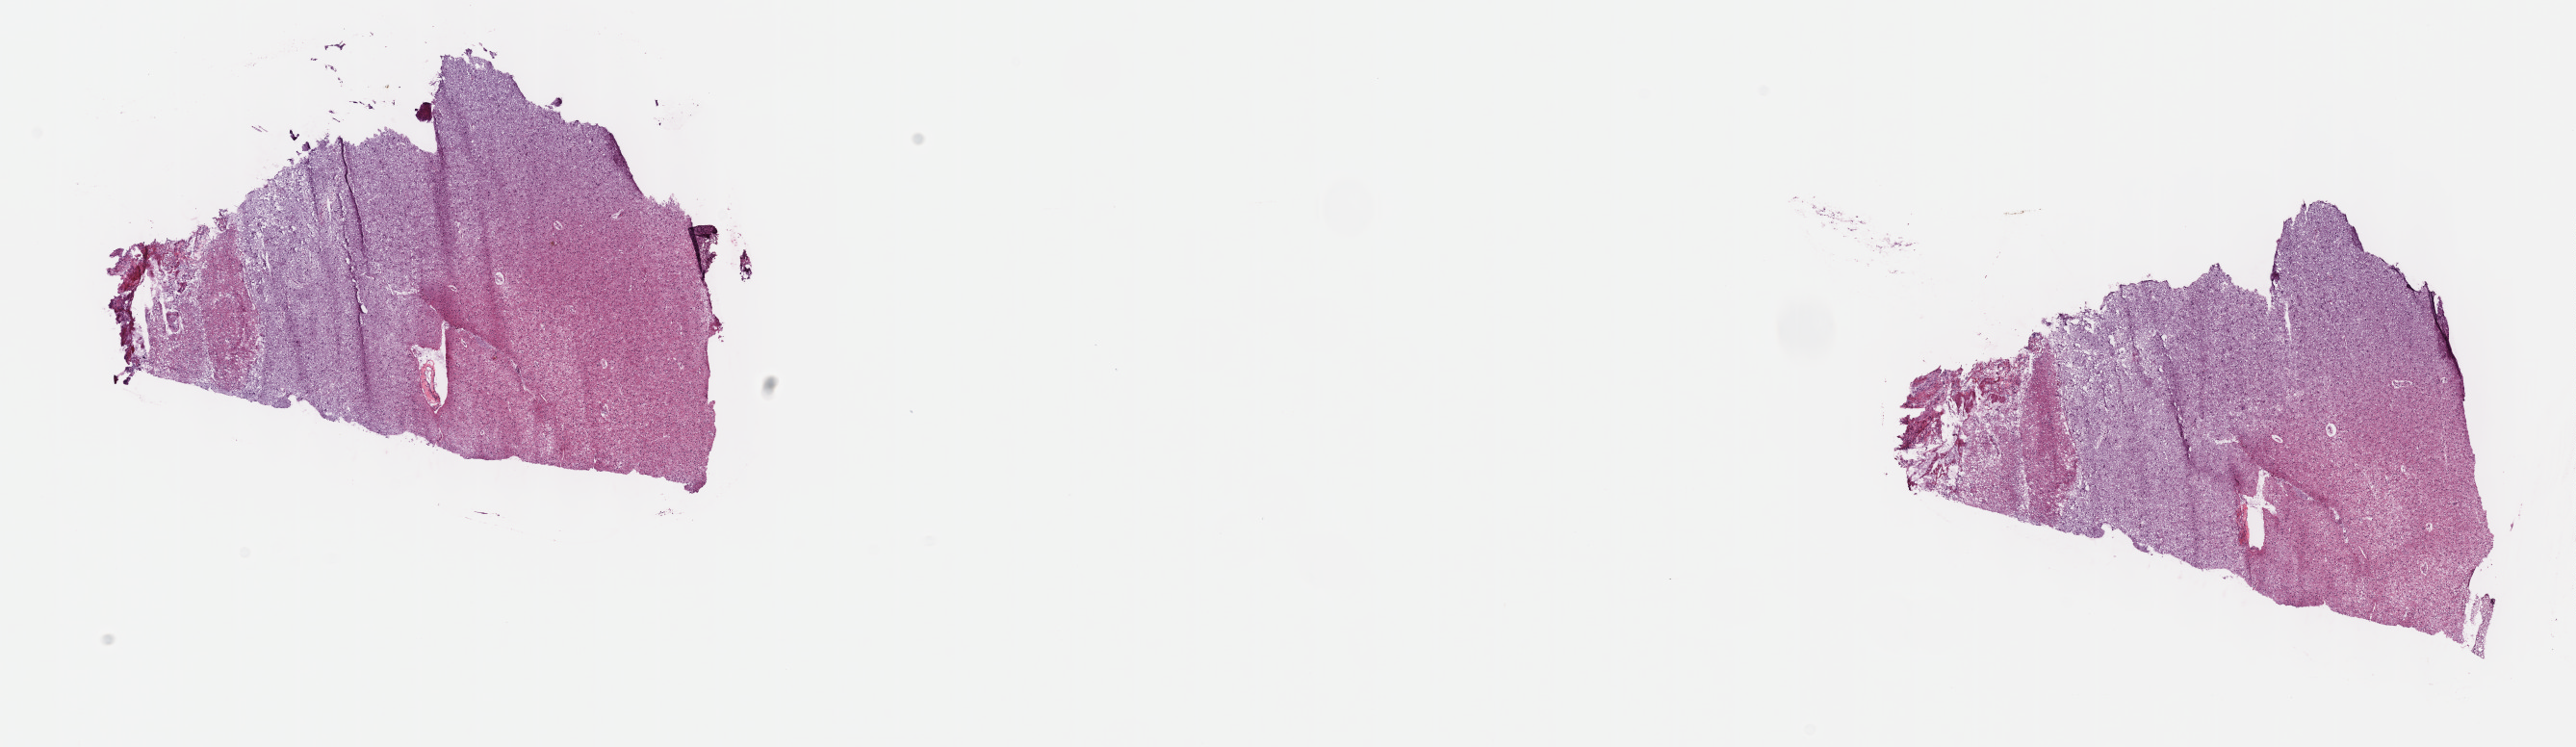
H&E whole-slide image, low-resolution overview of the scanned area, about 21.6 x 6.3 mm (from a 40x scan); frozen section; primary tumour sample from the brain. Male patient; age at initial diagnosis 40 years. Histologic grade: G2 (moderately differentiated). Composition of this section per pathologist review: tumour cells 40%, tumour nuclei 70%, normal cells 20%, stromal cells 40%, necrosis 0%. Inflammatory infiltration, as recorded: lymphocyte infiltration 0%, monocyte infiltration 0%, neutrophil infiltration 0%.
Histologic diagnosis: Oligodendroglioma, NOS. Laterality: right.